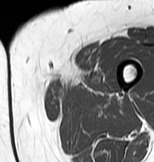
MRI of an extremity soft-tissue mass, one axial slice. MR volume resampled by the dataset authors to the PET/CT grid (not the native acquisition matrix). 154 × 162 image matrix, field of view 150 × 158 mm. Female patient. From the clinical record (not read from this slice): histological type: myxofibrosarcoma; grade: intermediate; site of the primary tumour: left thigh.
Structures marked on this image (expert contour drawn on MRI and transferred to this co-registered scan by the dataset authors):
- gross tumour volume including surrounding oedema: bounding box <51,68,109,97> (left, top, right, bottom; pixels)